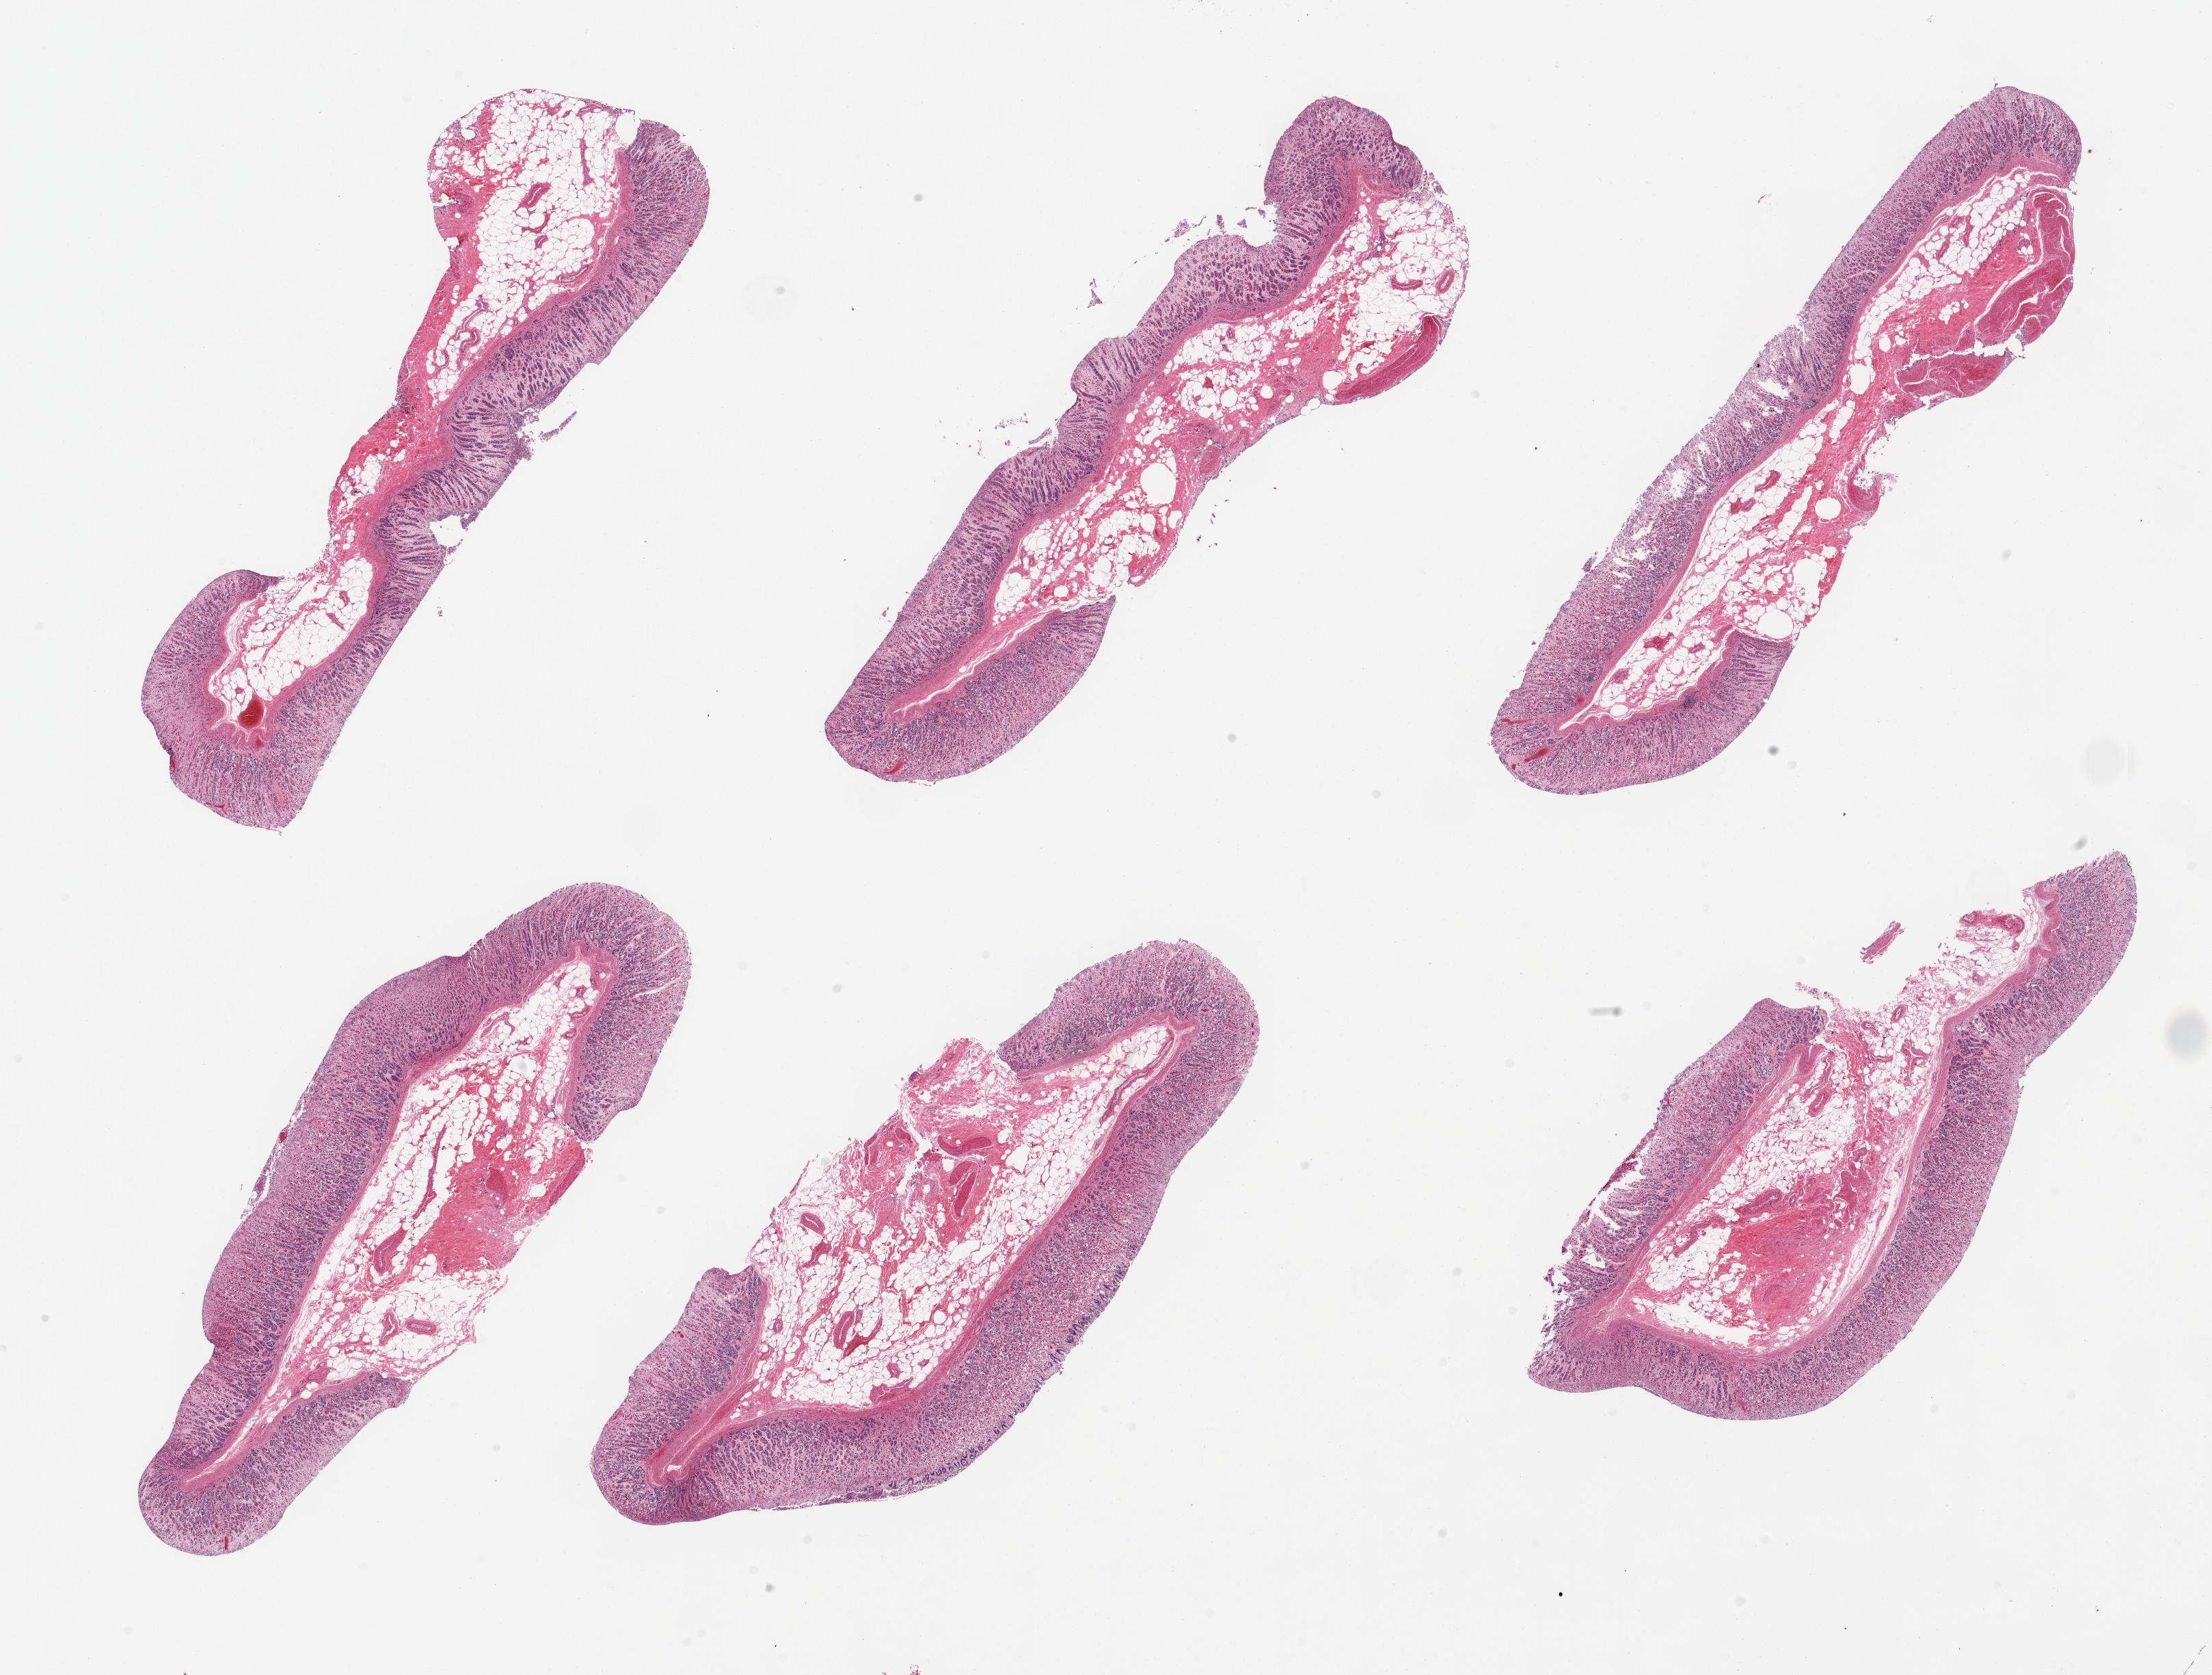
Hematoxylin and eosin (H&E) whole-slide image — a low-resolution overview of the entire scanned area, about 25.6 x 19.4 mm (acquisition: 20x scan). PAXgene-fixed paraffin-embedded (PFPE) section. Target tissue: stomach. Donor tissue sample.
Review note (as recorded): 6 pieces; autolyzed mucosa without muscularis.